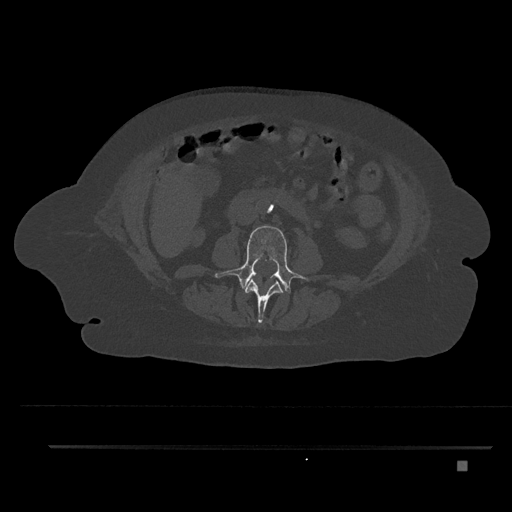
CT including the spine, one axial slice. Slice 141 of 797 in the series (ordered by position). Reconstruction kernel Br40s/3. 120 kVp. Bone window (W 1800 / L 400 HU). 0.5 mm slice thickness. 512 × 512 image matrix. Female patient, age 76 years. From the clinical record (not read from this slice): primary cancer: lung; vertebrae with lytic lesions (as recorded): T11, L3.
Outlined on this slice (semi-automatic segmentation, software-assisted and operator-edited):
- L2 vertebra: bounding box [x1, y1, x2, y2] px = [245, 278, 284, 324]
- L3 vertebra: [215, 225, 304, 294]